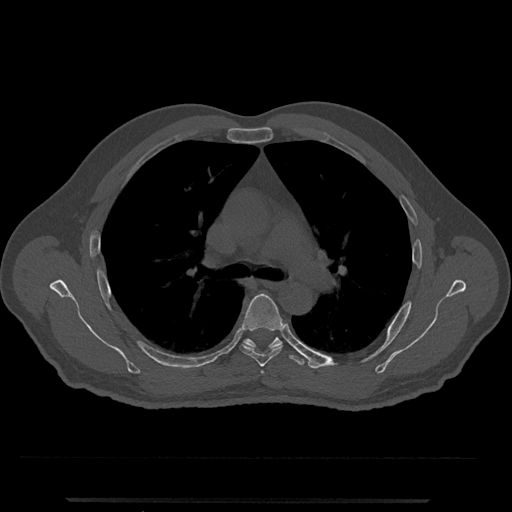
CT including the spine, one axial slice; position 775 of 797 along the scan axis; reconstruction kernel Br40s/3; bone window (W 1800 / L 400 HU); 0.5 mm slice thickness; 512 × 512 image matrix, field of view 419 × 419 mm. Male patient, age 63 years. From the clinical record (not read from this slice): primary cancer: prostate.
Structures marked on this image (semi-automatically segmented with operator editing):
- T5 vertebra: bounding box [x1, y1, x2, y2] px = [239, 293, 283, 367]
- T6 vertebra: [243, 337, 305, 366]